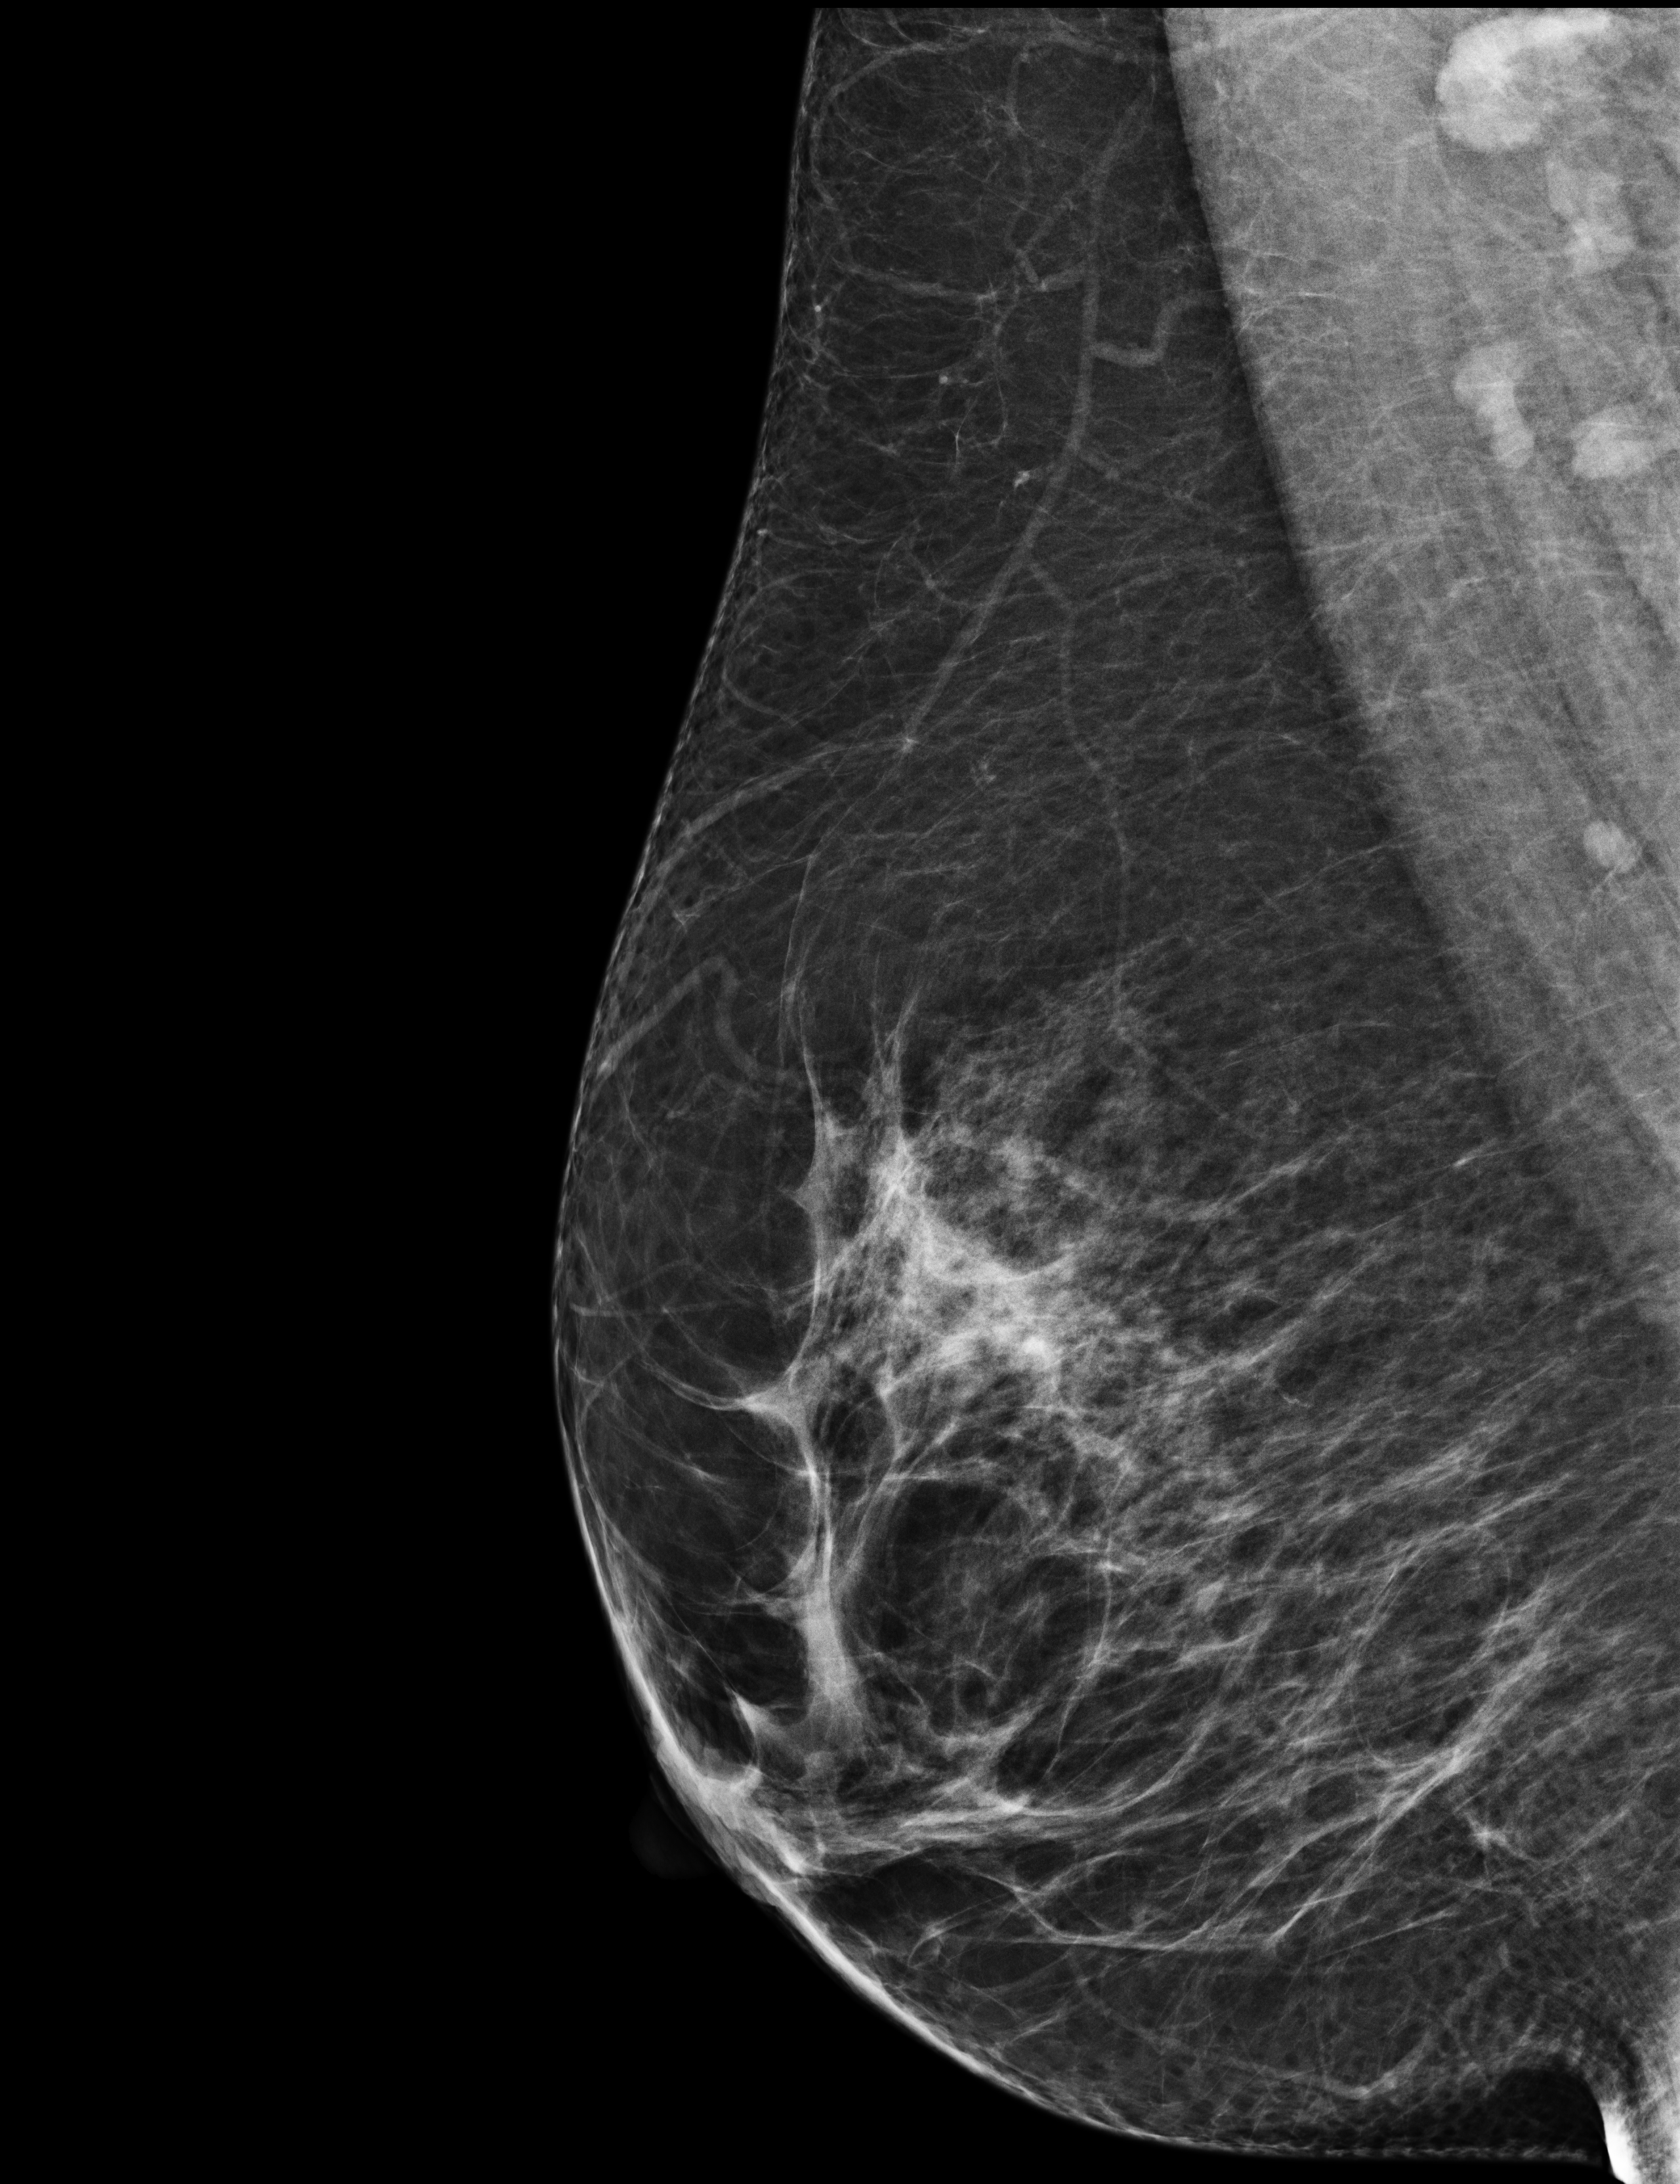
Annual screening mammography examination, compressed breast thickness 82 mm, system: Selenia Dimensions. Female patient, age 57 years.
Image type: full-field digital mammogram. Breast: right. Projection: medio-lateral oblique projection.